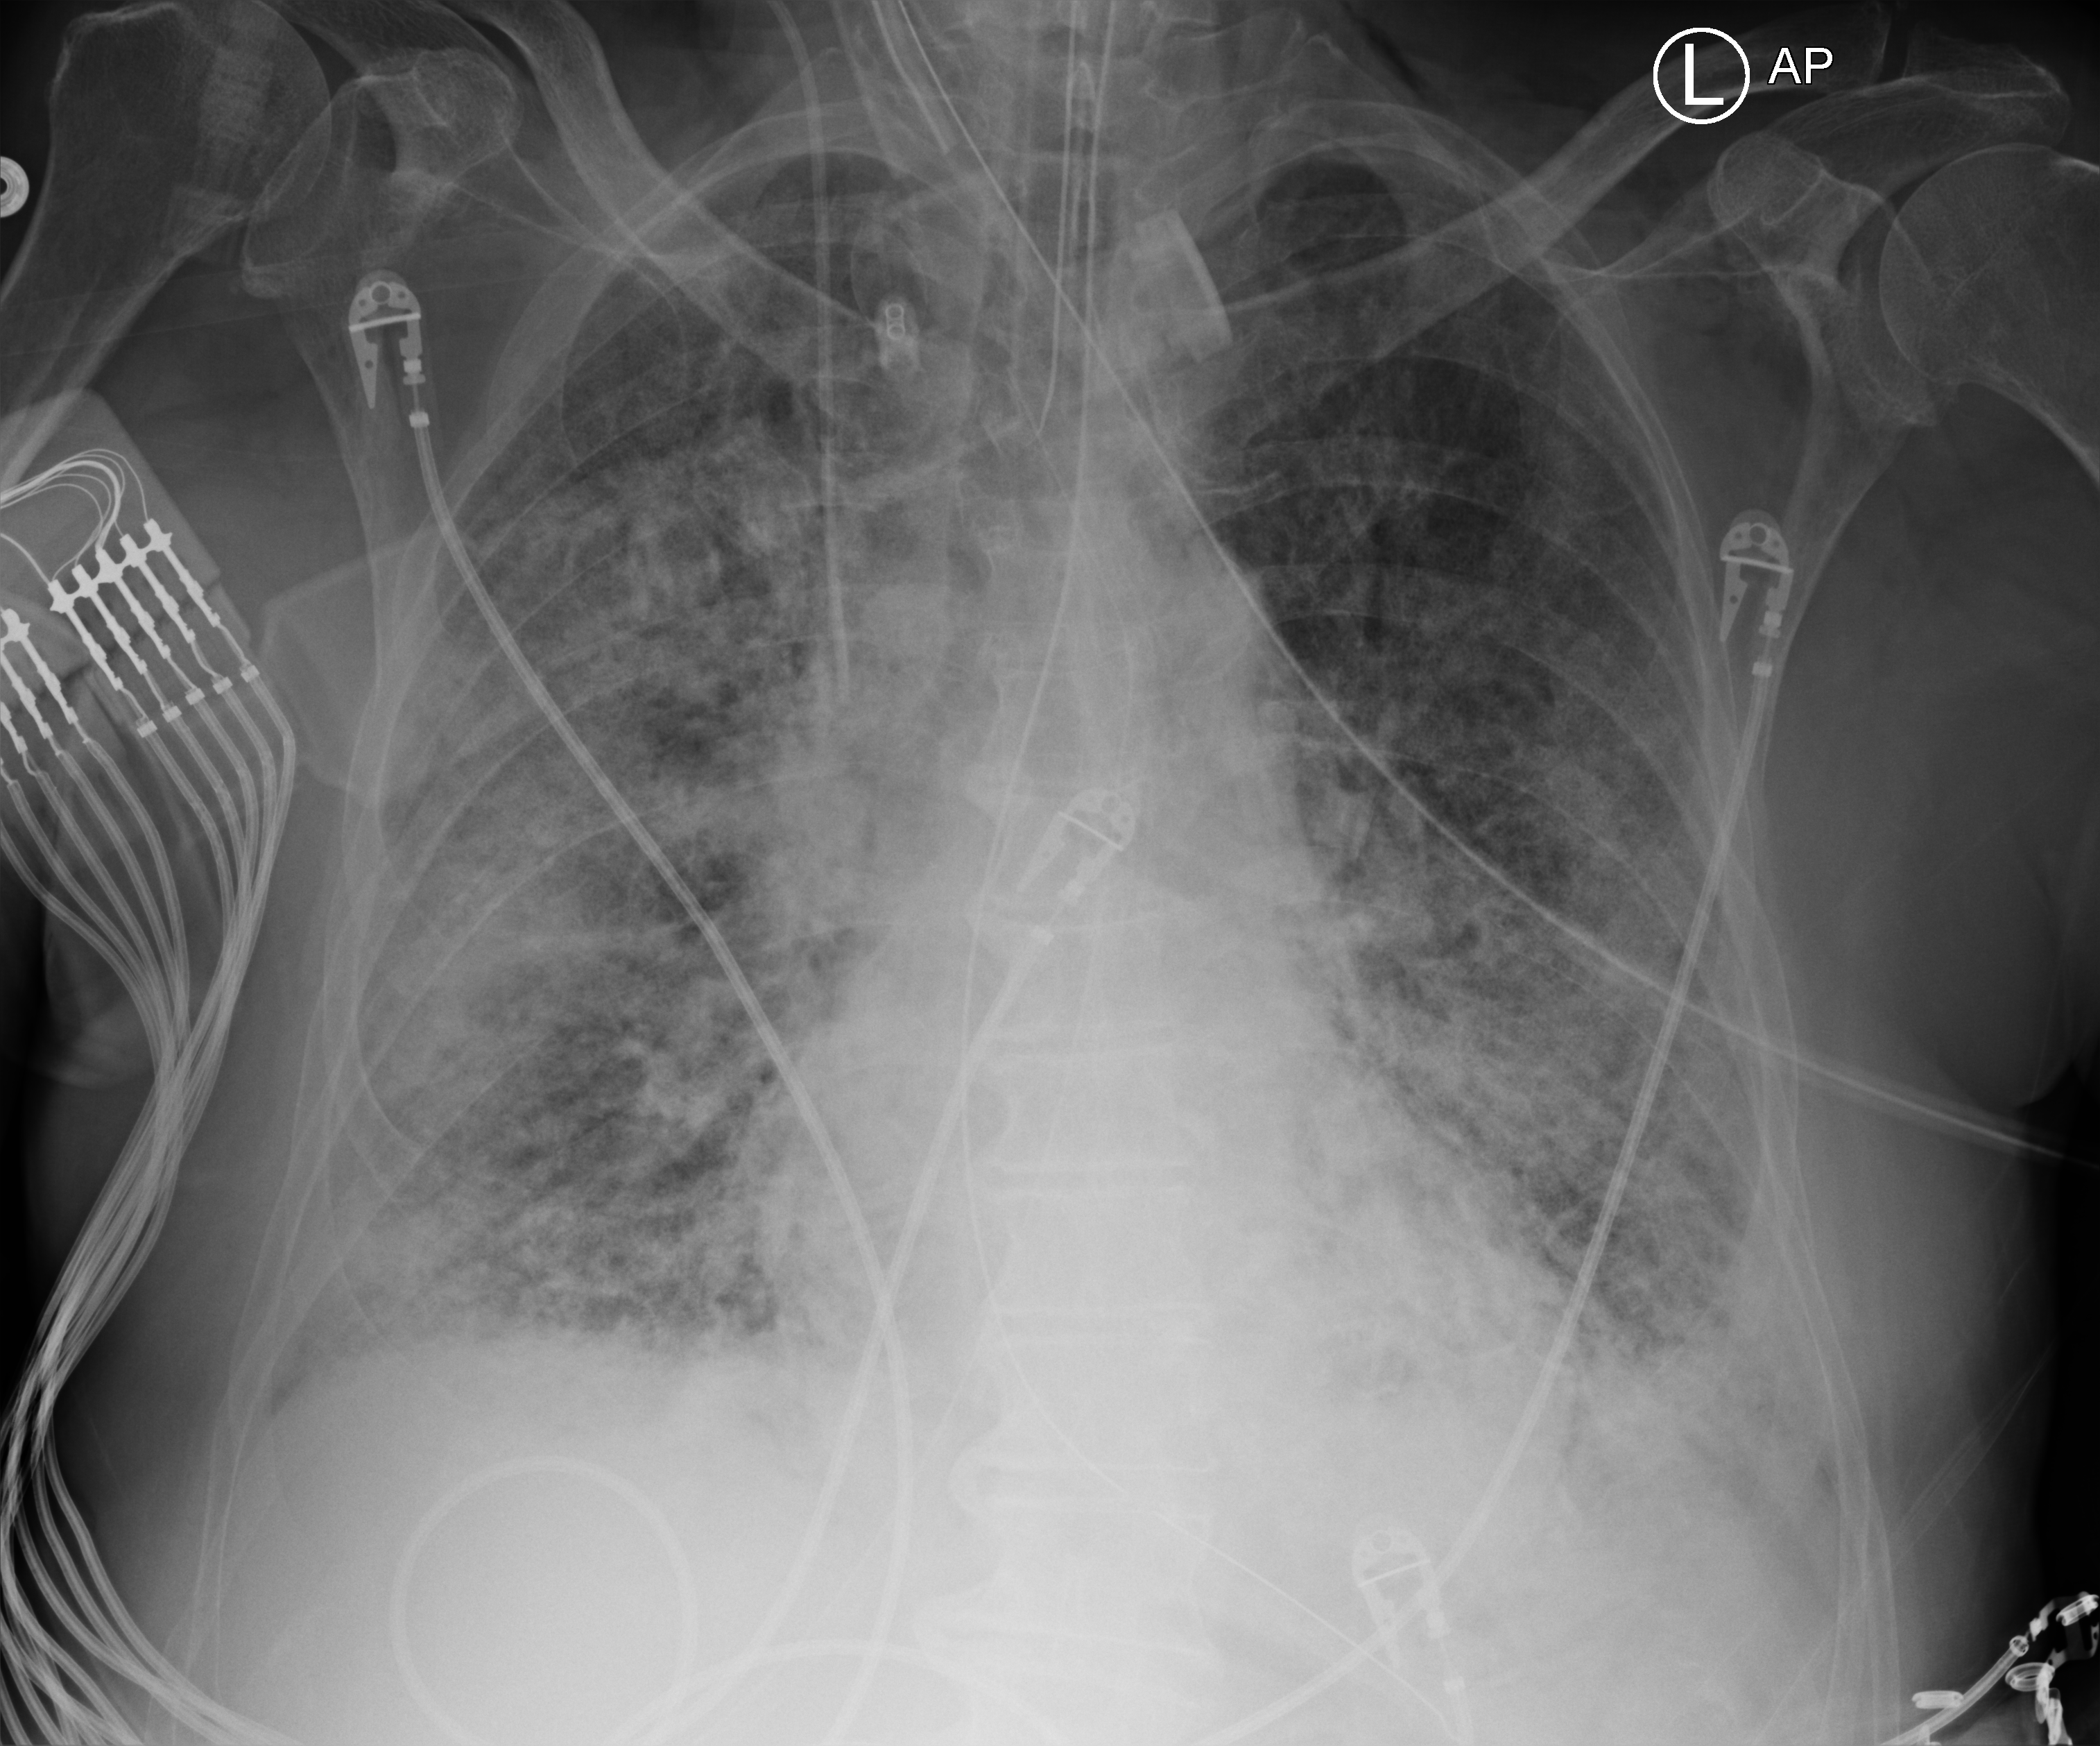
Chest X-ray (portable); anteroposterior (AP) projection. Patient hospitalised with COVID-19; male, aged 75–90 years.
Admission-level facts for this patient (not findings on this image; timing relative to this image not recorded): mechanically ventilated during this hospital stay: yes.